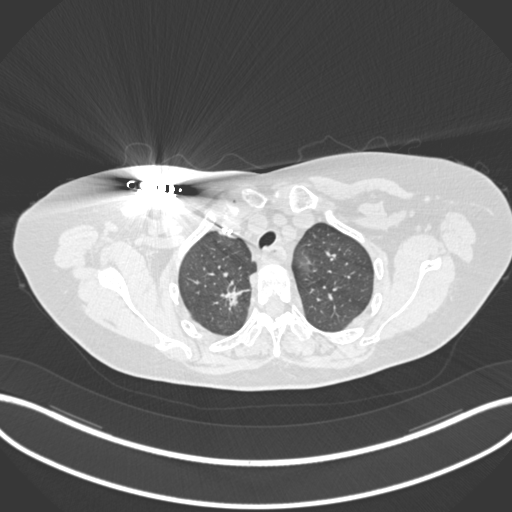
Chest CT, one axial slice. Slice 149 of 176 in the series (ordered by position). Reconstruction kernel B30f. Lung window (W 1500 / L -600 HU). 1 mm slice thickness. 512 × 512 image matrix. Female patient, age 72 years. Case-level facts recorded for this patient, not image findings: clinical TNM (as recorded): T1c N0 M0.
Annotated regions visible in this slice (bounding box drawn by a radiologist):
- lung tumour (recorded histology: adenocarcinoma): bounding box [x1, y1, x2, y2] px = [216, 282, 250, 311]